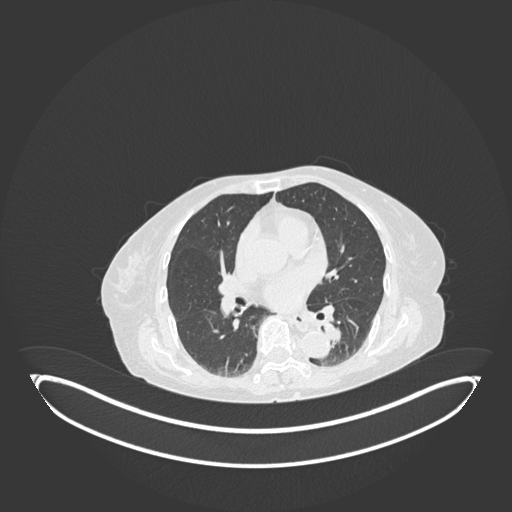
Chest CT, one axial slice; slice 62 of 189 in the series (ordered by position); reconstruction kernel B30f; 120 kVp; lung window (W 1500 / L -600 HU); 1 mm slice thickness; 512 × 512 image matrix, field of view 500 × 500 mm. Female patient, age 82 years. Case-level facts recorded for this patient, not image findings: clinical TNM (as recorded): T1b N0 M1.
Structures marked on this image (rectangle marked by the reading radiologist):
- lung tumour (recorded histology: adenocarcinoma): bounding box <323,321,348,349> (left, top, right, bottom; pixels)